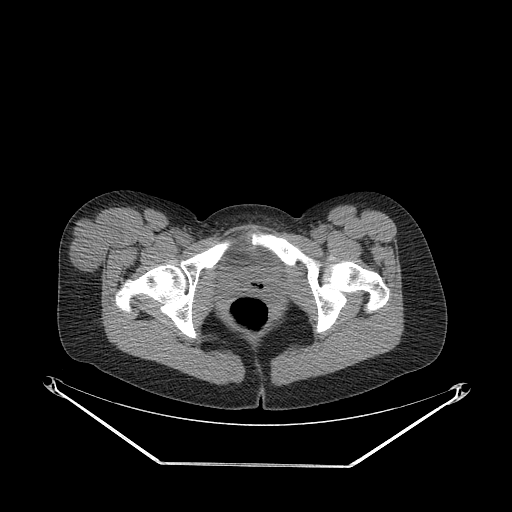
CT of an extremity soft-tissue mass (from a PET/CT study), one axial slice. Position 63 of 267 along the scan axis. Reconstruction kernel STANDARD. 140 kVp. Soft-tissue window (W 400 / L 40 HU). 512 × 512 image matrix, field of view 500 × 500 mm. Female patient. From the clinical record (not read from this slice): histological type: synovial sarcoma; grade: intermediate; site of the primary tumour: right thigh.
Annotated regions visible in this slice (expert contour drawn on MRI and transferred to this co-registered scan by the dataset authors):
- gross tumour volume including surrounding oedema: bounding box (x1, y1, x2, y2) in pixels: (69, 212, 124, 273)
- gross tumour volume (mass): (69, 212, 124, 273)